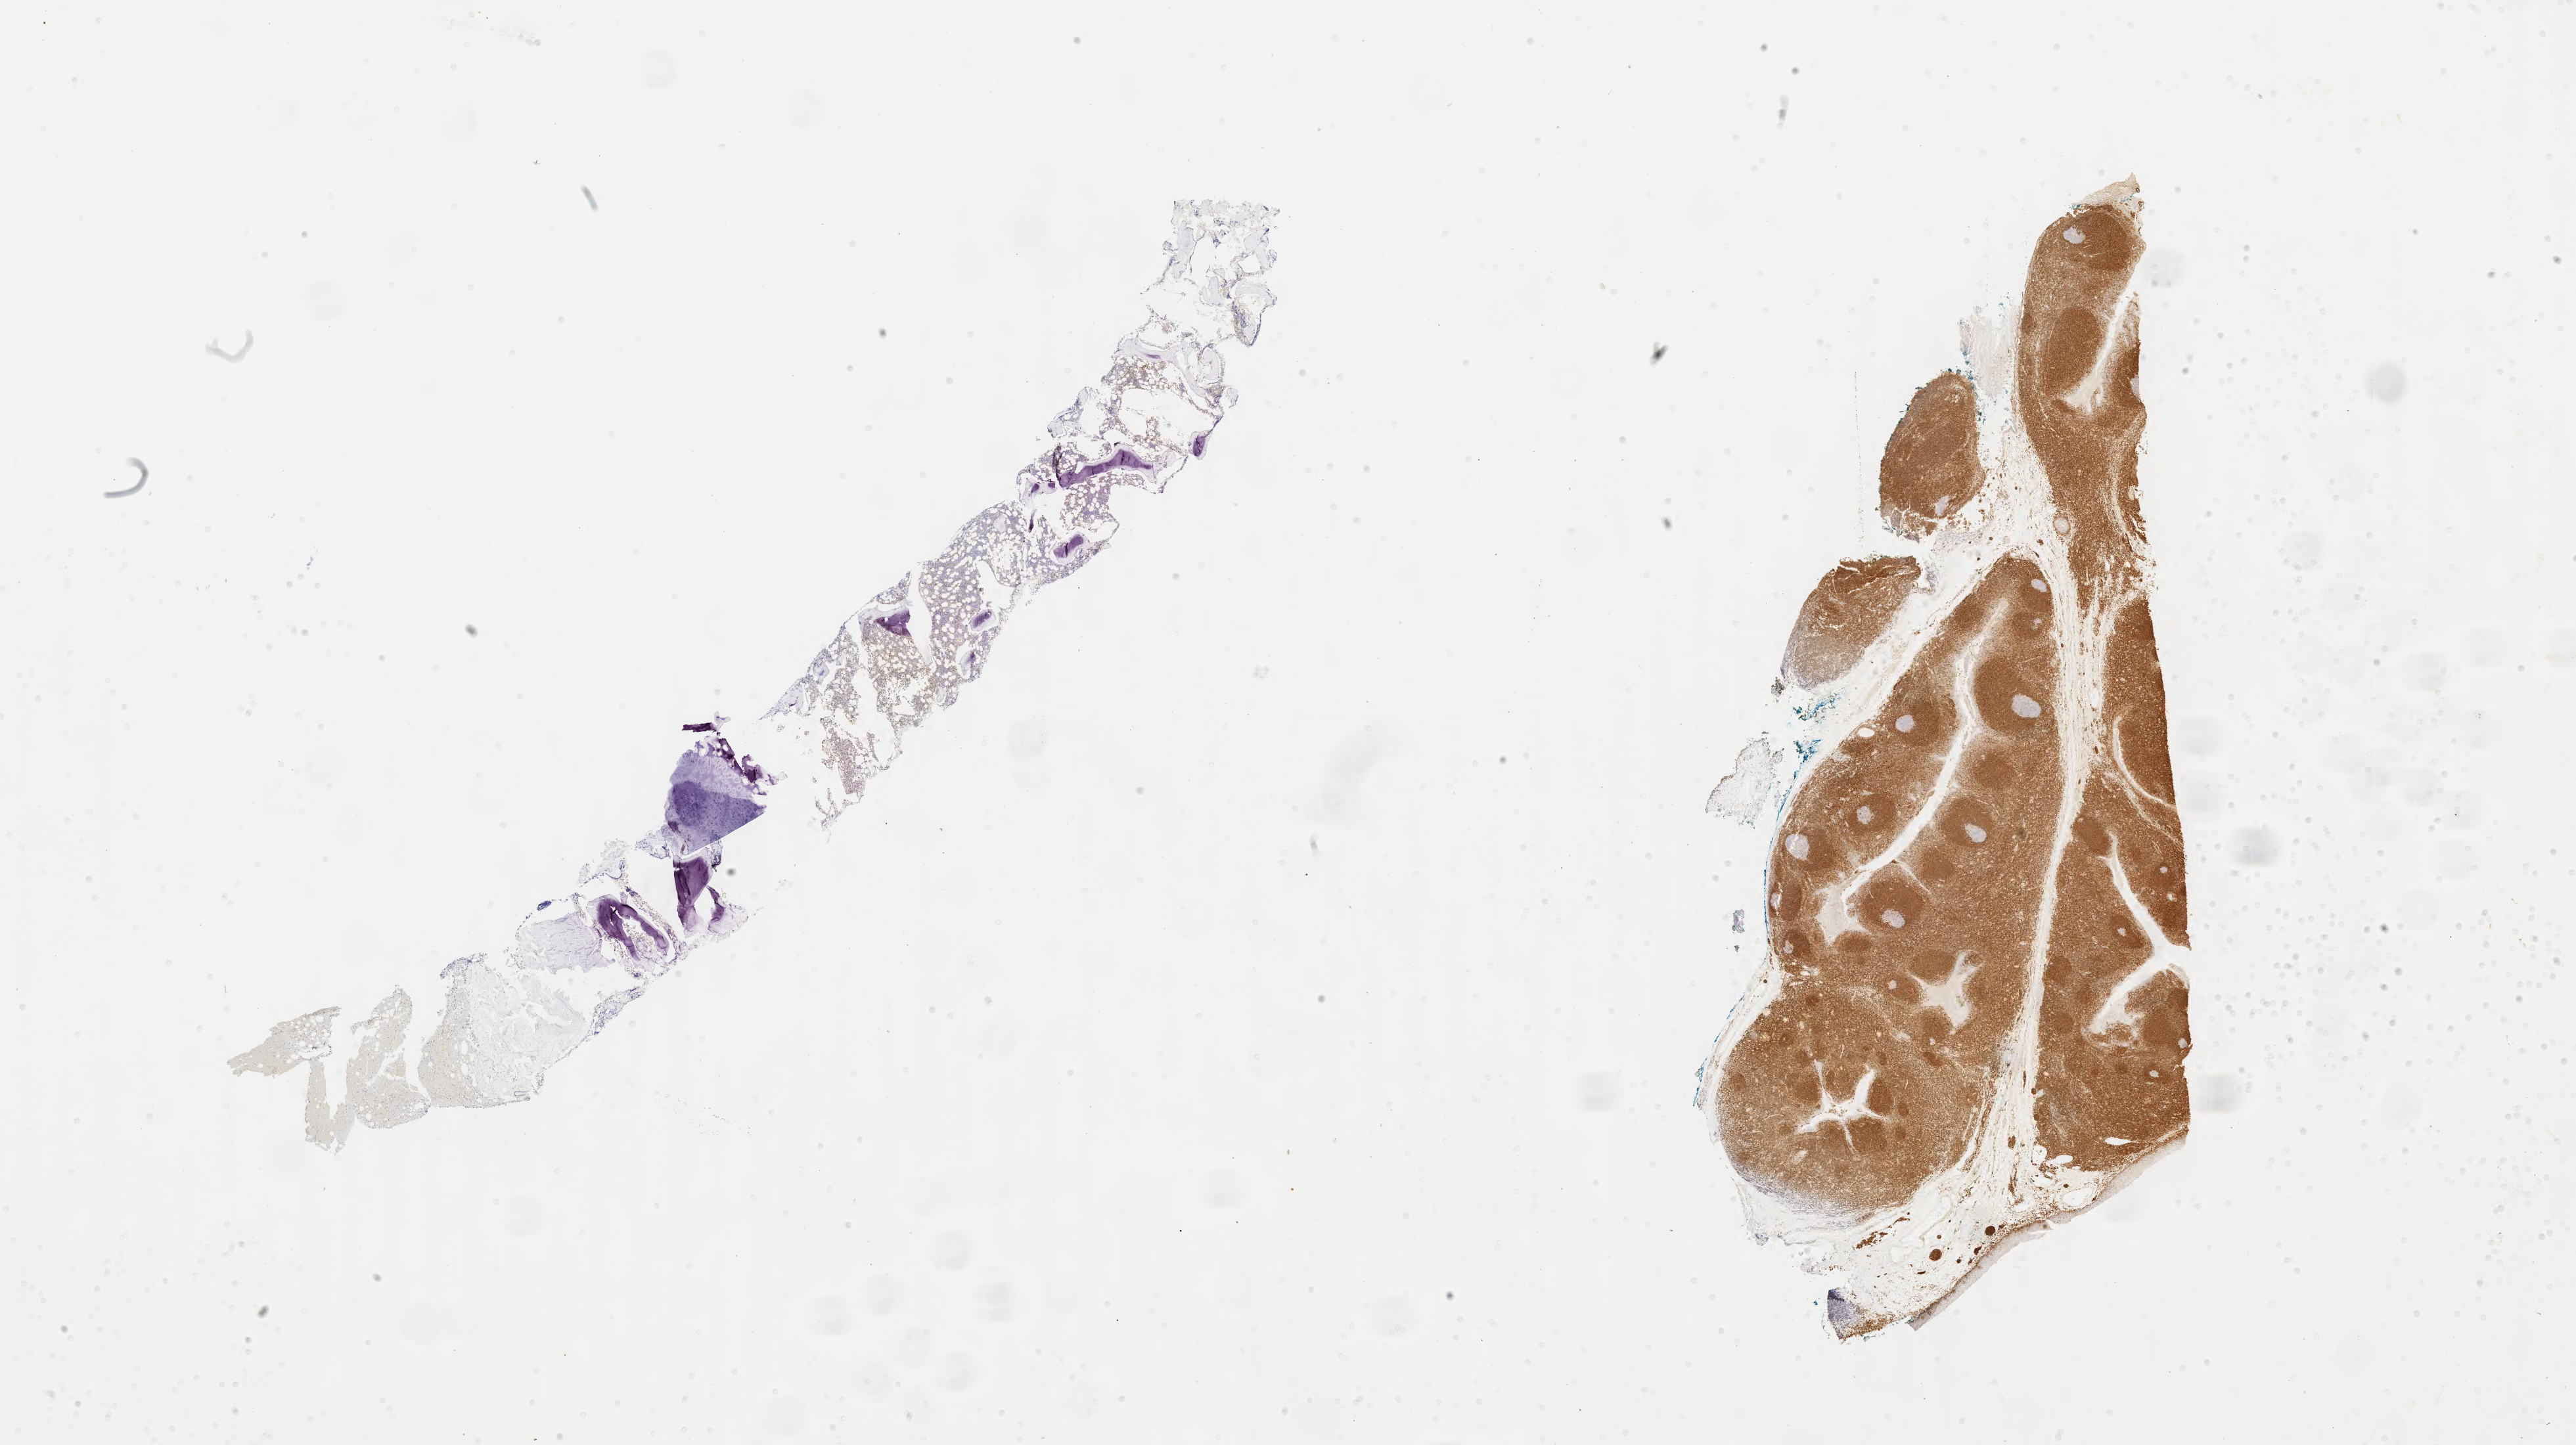
Whole-slide image, immunohistochemical stain for BCL2 — a low-resolution overview of the entire scanned area, about 31.7 x 17.8 mm. Tumor tissue. Anatomic site: bone marrow. Patient: male, 15 years old.
Diagnosis: Burkitt lymphoma, NOS.